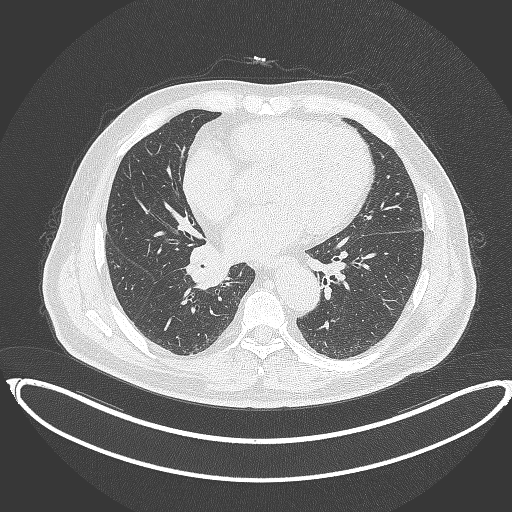
Chest CT, one axial slice; slice 181 of 387 in the series (ordered by position); 120 kVp; lung window (W 1500 / L -600 HU); 1 mm slice thickness; 512 × 512 image matrix, field of view 448 × 448 mm. Patient: male, 61 years. Case-level facts recorded for this patient, not image findings: clinical TNM (as recorded): T1b N1 M0.
Outlined on this slice (bounding box drawn by a radiologist):
- lung tumour (recorded histology: squamous cell carcinoma): bounding box <185,242,231,291> (left, top, right, bottom; pixels)